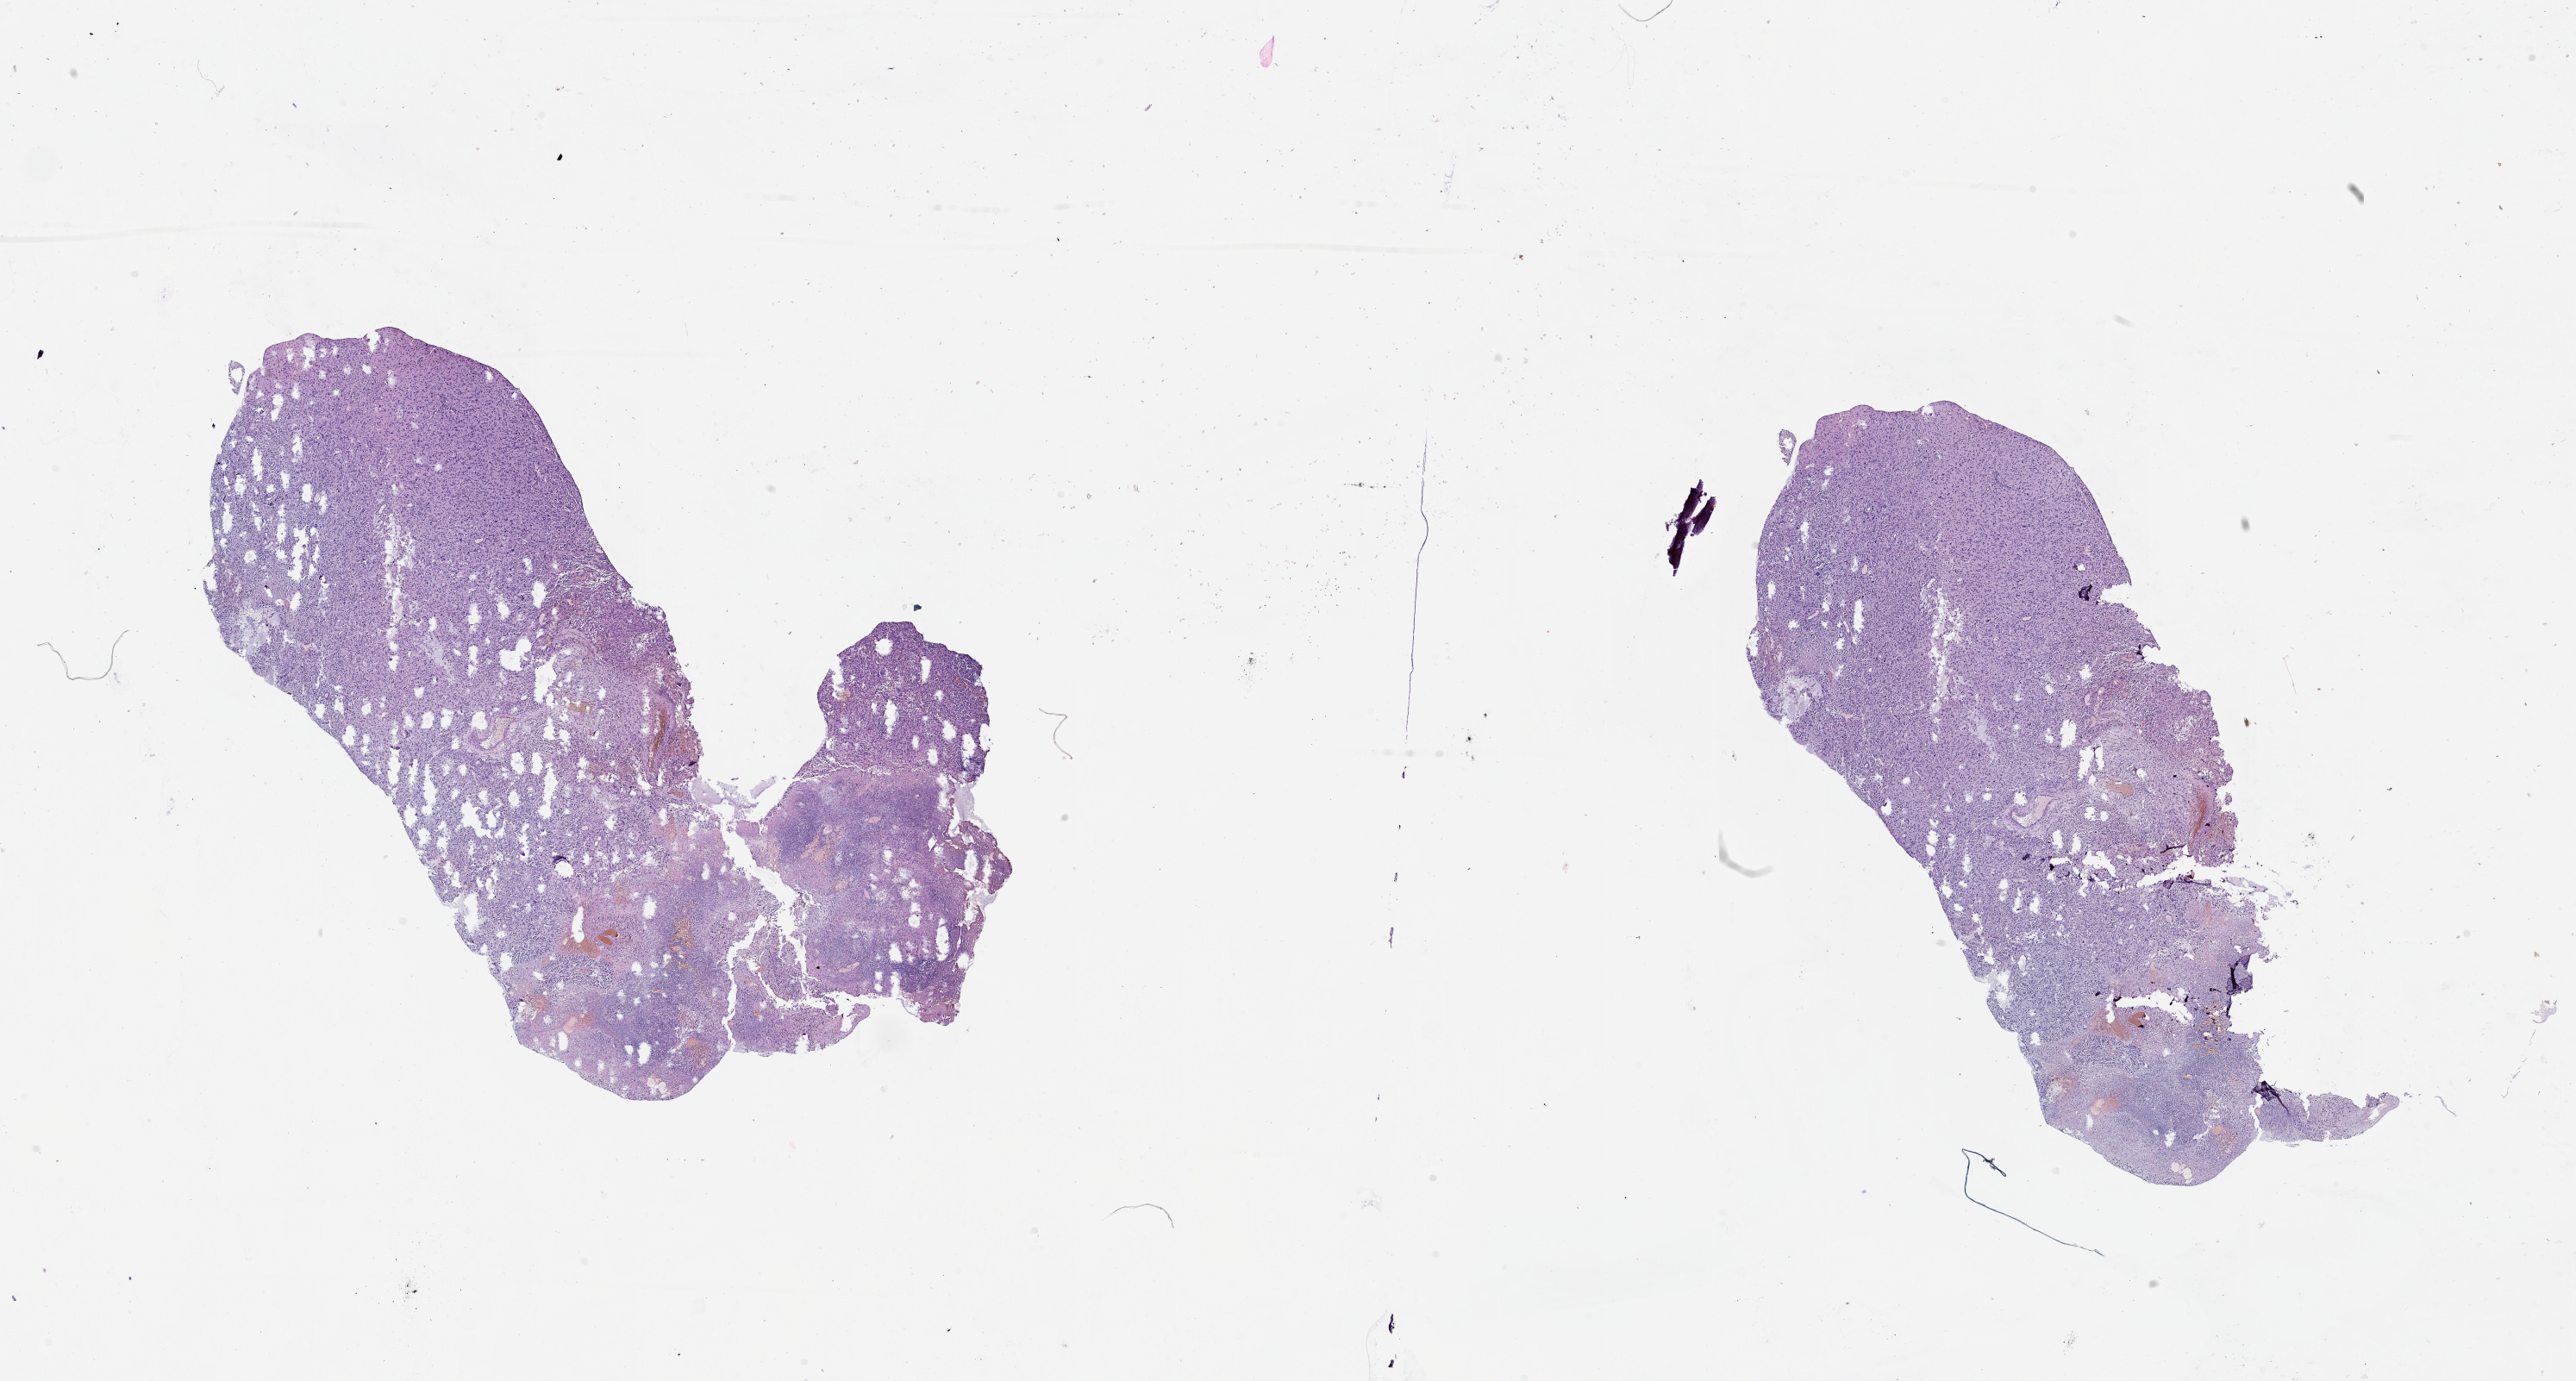
Digitized H&E-stained tissue section (whole slide) — shown as a low-resolution overview of the whole scanned area (about 24.1 x 12.9 mm). Tumour tissue sample, sampled site: frontal lobe. Male, 63 y/o. Slide review estimates, as recorded: tumour nuclei 80%, necrosis 25%.
- primary tumour site (as recorded): frontal lobe
- diagnosis: Glioblastoma